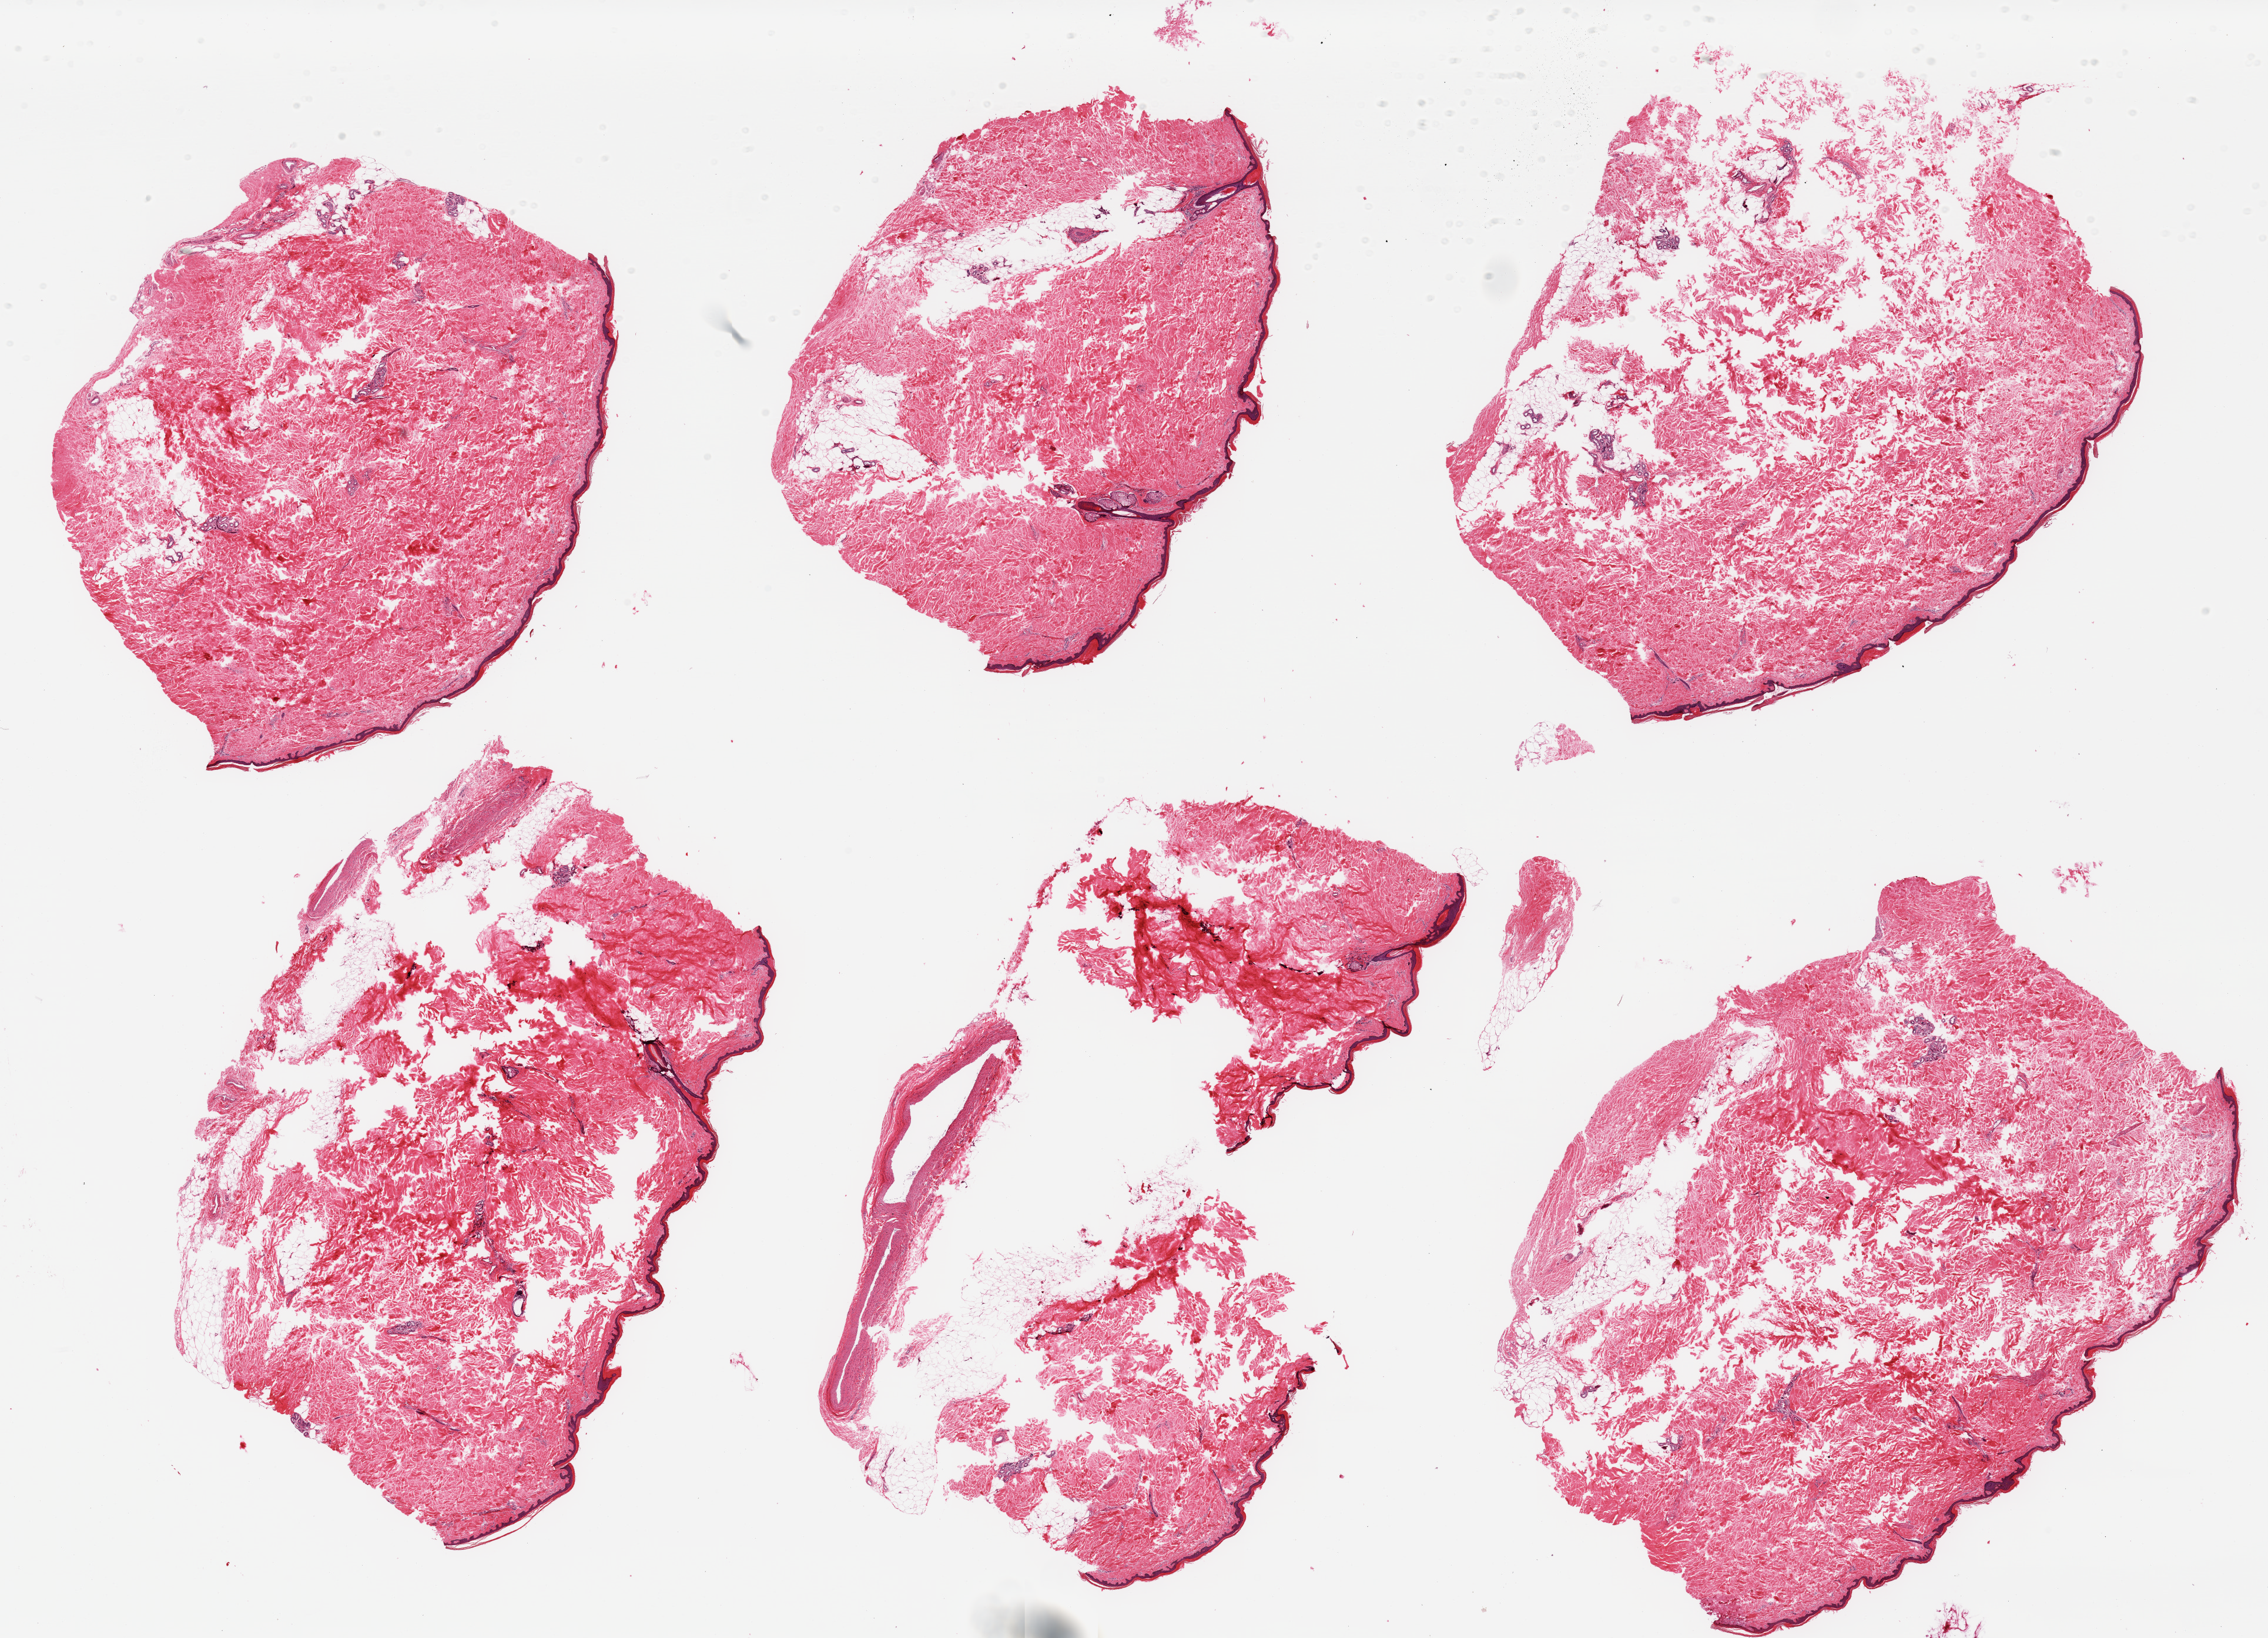
Haematoxylin and eosin whole-slide image — a low-resolution overview of the entire scanned area, about 30.5 x 22.0 mm (from a 20x scan); PAXgene-fixed, paraffin-embedded tissue; sampled site (target tissue): skin of lower leg; tissue donor sample.
Review note (as recorded): 6 pieces, moderate dermal fat; squamous epithelium is ~40 microns.